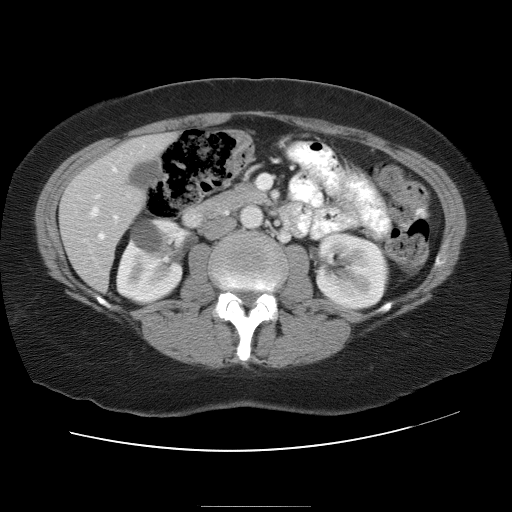
Contrast-enhanced abdominal CT, one axial slice. Slice 12 of 30 in the series (ordered by position). Reconstruction kernel STANDARD. 120 kVp. Intravenous contrast given. Soft-tissue window (W 400 / L 40 HU). 512 × 512 image matrix. Female patient, age 52 years. From the clinical record (not read from this slice): diagnosis: colorectal cancer liver metastases, imaged before liver resection.
Structures marked on this image (expert manual segmentation):
- hepatic veins: bounding box <90,208,98,217> (left, top, right, bottom; pixels)
- liver: <60,134,174,289>
- planned liver remnant (the part of the liver to remain after resection): <168,136,174,140>
- portal vein (with intrahepatic branches): <95,168,117,239>